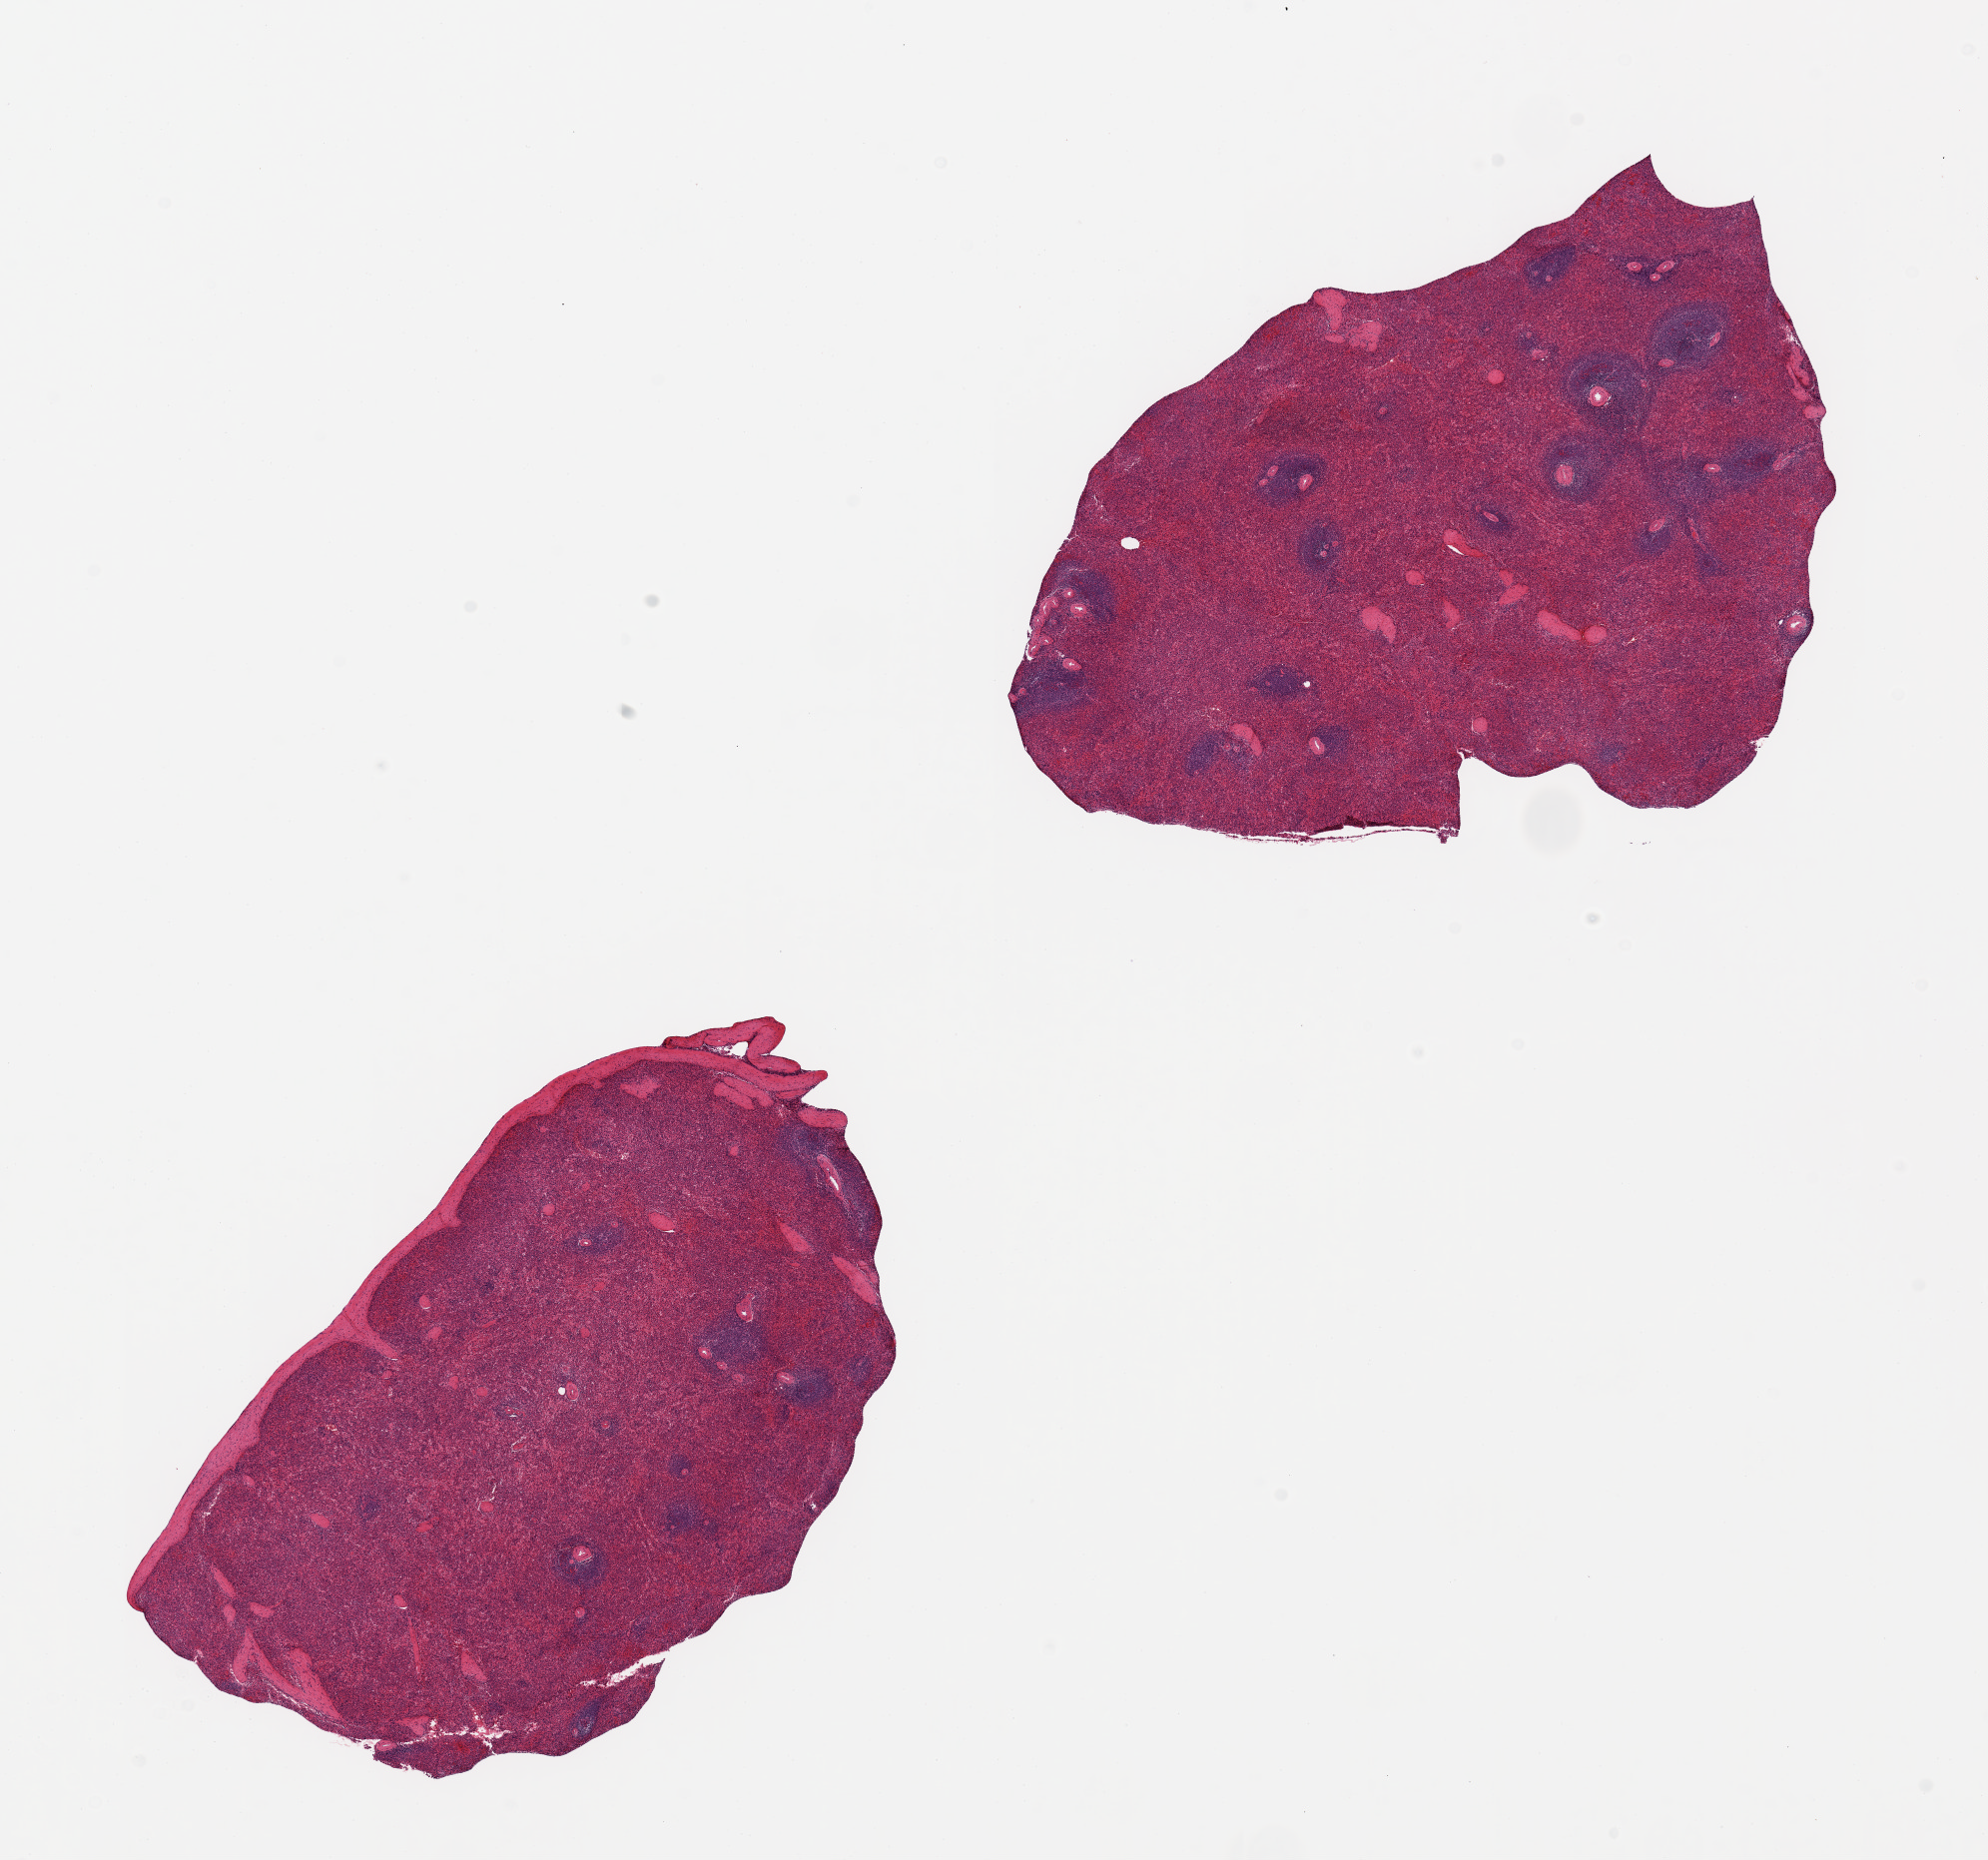
Hematoxylin and eosin (H&E) whole-slide image, brightfield, low-resolution overview of the scanned area, about 15.8 x 14.7 mm (from a 20x scan). PAXgene-fixed paraffin-embedded (PFPE) section. Section of spleen (target tissue). Tissue donor sample. Male donor.
Reviewer comment on this tissue sample: 2 pieces, 7x5 & 6.5x4mm; polymorphs present in some areas.